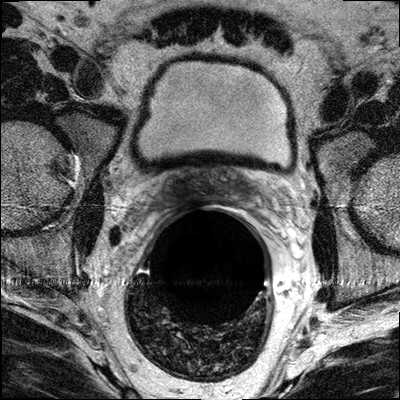
MRI of the prostate; 3 images, each a single mid-volume slice chosen by position (not for content). Treatment context recorded for this patient: No surgery, radiation theraphy.
Image 1: axial T2-weighted image, series "T2W_TSE_AX", slice 17 of 32.
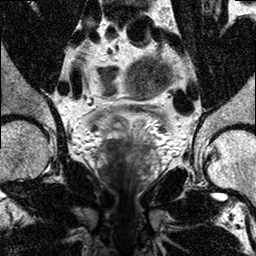
Image 2: T2-weighted coronal slice, series "T2W_TSE_COR", slice 13 of 24.
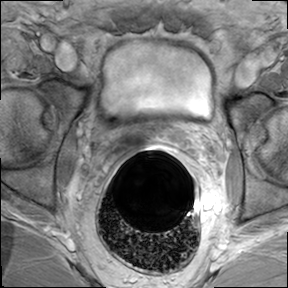
Image 3: axial dynamic contrast-enhanced (DCE) T1-weighted image, series "AX BLISS_GAD_8", slice 17 of 32, dynamic phase 5 of 8, 6 mm slice thickness.
Radiologist's MRI report for this examination:
The prostate has a maximal lateral diameter of 4.7 cm, a maximal craniocaudal diameter of 4.6 cm and a maximal AP diameter of 2.6 cm resulting in an estimated gland volume of 29 cc. The zonal anatomy is preserved. There is T2-hypointense signal seen in the posterior and posterior lateral peripheral zone, mid third and apical third, bilateral.(more on the left). Largest dominant nodule on the left is 11 x 13 mm at 5 o'clock apical peripheral zone; the largest dominant nodule on the right is seen in at 8 o'clock mid third of the prostate (also peripheral zone) measuring 7 x 6 mm. These areas show suspicious enhancement curves on the dynamic series. No evidence for involvement of the neurovascular bundle on either side.No evidence for seminal vesicles infiltration. No evidence of involvement of bladder neck and rectal wall. No suspiciously enlarged obturator and iliac lymph nodes.IMPRESSION: Bilateral (left more than right) prostate cancer in the midthird and apical third of the prostate within the peripheral zones. No MRI evidence of extraprostatic extension.

Prostate biopsy pathology (as recorded):
Gross Description: The specimen consists of multiple core fragments of tan soft tissue measuring 1.4cm to 1.9cm in length and 0.1cm in circumference. The specimen is submitted entirely in six cassettes. PROSTATE: 1-RIGHT PZ: PROSTATE TISSUE WITH FOCAL CHRONIC INFLAMMATION. NO TUMOR IDENTIFIED. 2-RIGHT PZ/TZ: PROSTATIC ADENOCARCINOA, GLEASON SCORE 3+4+7/10, INVOLVING 25% OF THE TISSUE REPRESENTED. 3-RIGHT APEX: PROSTATIC ADENOCARCINOMA, GLEASON SCORE 3+3=6/10, INVOLVING 1% OF THE TISSUE REPRESENTED. 4-LEFT PZ: PROSTATIC ADENOCARCINOMA, GLEASON SCORE 3+4=7/10, INVOLVING 60% OF THE TISSUE REPRESENTED. 5-LEFT PZ/TZ: PROSTATIC ADENOCARCINOMA, GLEASON SCORE 3+4=7/10, INVOLVING 70% OF THE TISSUE REPRESENTED. 6-LEFT APEX: PROSTATIC ADENOCARCINOMA, GLEASON SCORE 3+3=6/10, INVOLVING 40% OF THE TISSUE REPRESENTED.